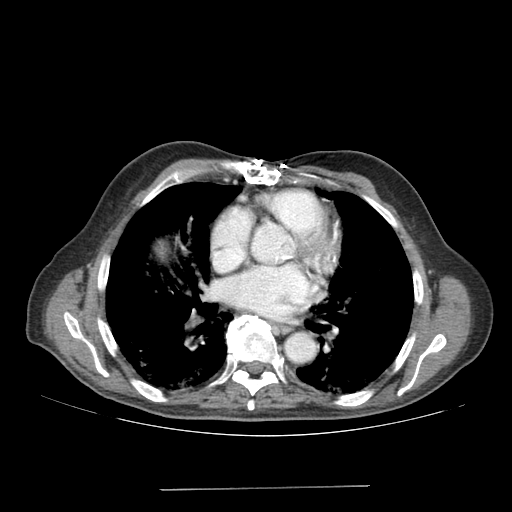
Contrast-enhanced abdominal CT (liver protocol), one axial slice. Position 182 of 192 along the scan axis. 120 kVp. Soft-tissue window (W 400 / L 40 HU). 2.5 mm slice thickness. 512 × 512 image matrix, field of view 400 × 400 mm. From the clinical record (not read from this slice): diagnosis: hepatocellular carcinoma (patient treated with transarterial chemoembolisation; whether this scan precedes or follows treatment is not stated here); TNM stage (as recorded): Stage-IVA; Child-Pugh class: A; tumour differentiation: poorly differentiated.
Outlined on this slice (semi-automatic segmentation, software-assisted and operator-edited):
- liver parenchyma outside the tumour (the mass and vessels are separate outlines, so this box may not span the whole liver): box from (x=156, y=240) to (x=168, y=259) px